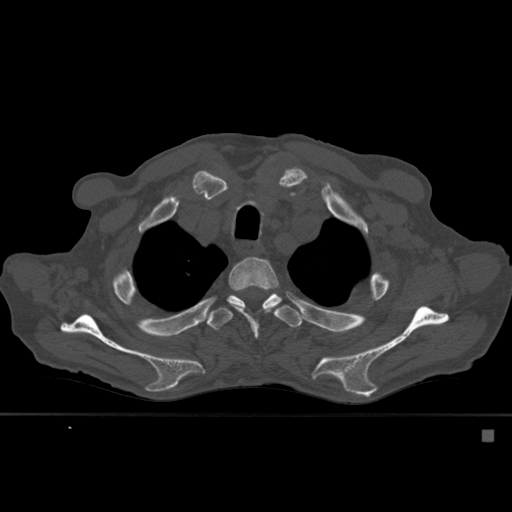
CT including the spine, one axial slice; bone window (W 1800 / L 400 HU); 512 × 512 image matrix, field of view 373 × 373 mm. Patient: male, 78 years. From the clinical record (not read from this slice): primary cancer: prostate.
Outlined on this slice (semi-automatic segmentation, software-assisted and operator-edited):
- T3 vertebra: bounding box [x1, y1, x2, y2] px = [228, 257, 280, 337]
- T4 vertebra: [207, 286, 302, 330]